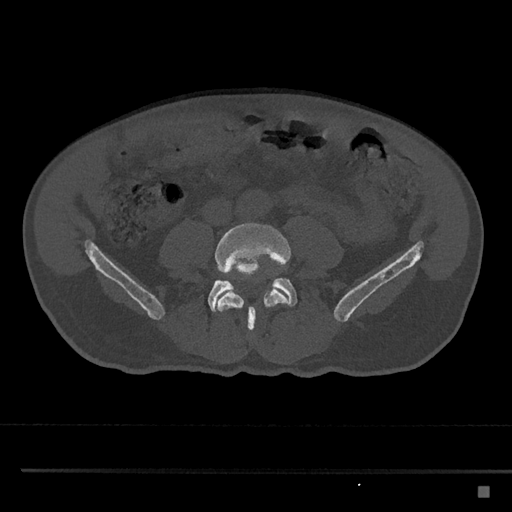
CT including the spine, one axial slice. Position 612 of 797 along the scan axis. 120 kVp. Bone window (W 1800 / L 400 HU). 0.5 mm slice thickness. 512 × 512 image matrix, field of view 391 × 391 mm. Patient: male, 59 years. Case-level facts recorded for this patient, not image findings: primary cancer: prostate.
Annotated regions visible in this slice (semi-automatic segmentation, software-assisted and operator-edited):
- L4 vertebra: box from (x=214, y=222) to (x=291, y=332) px
- L5 vertebra: (x=208, y=271)–(x=298, y=312)